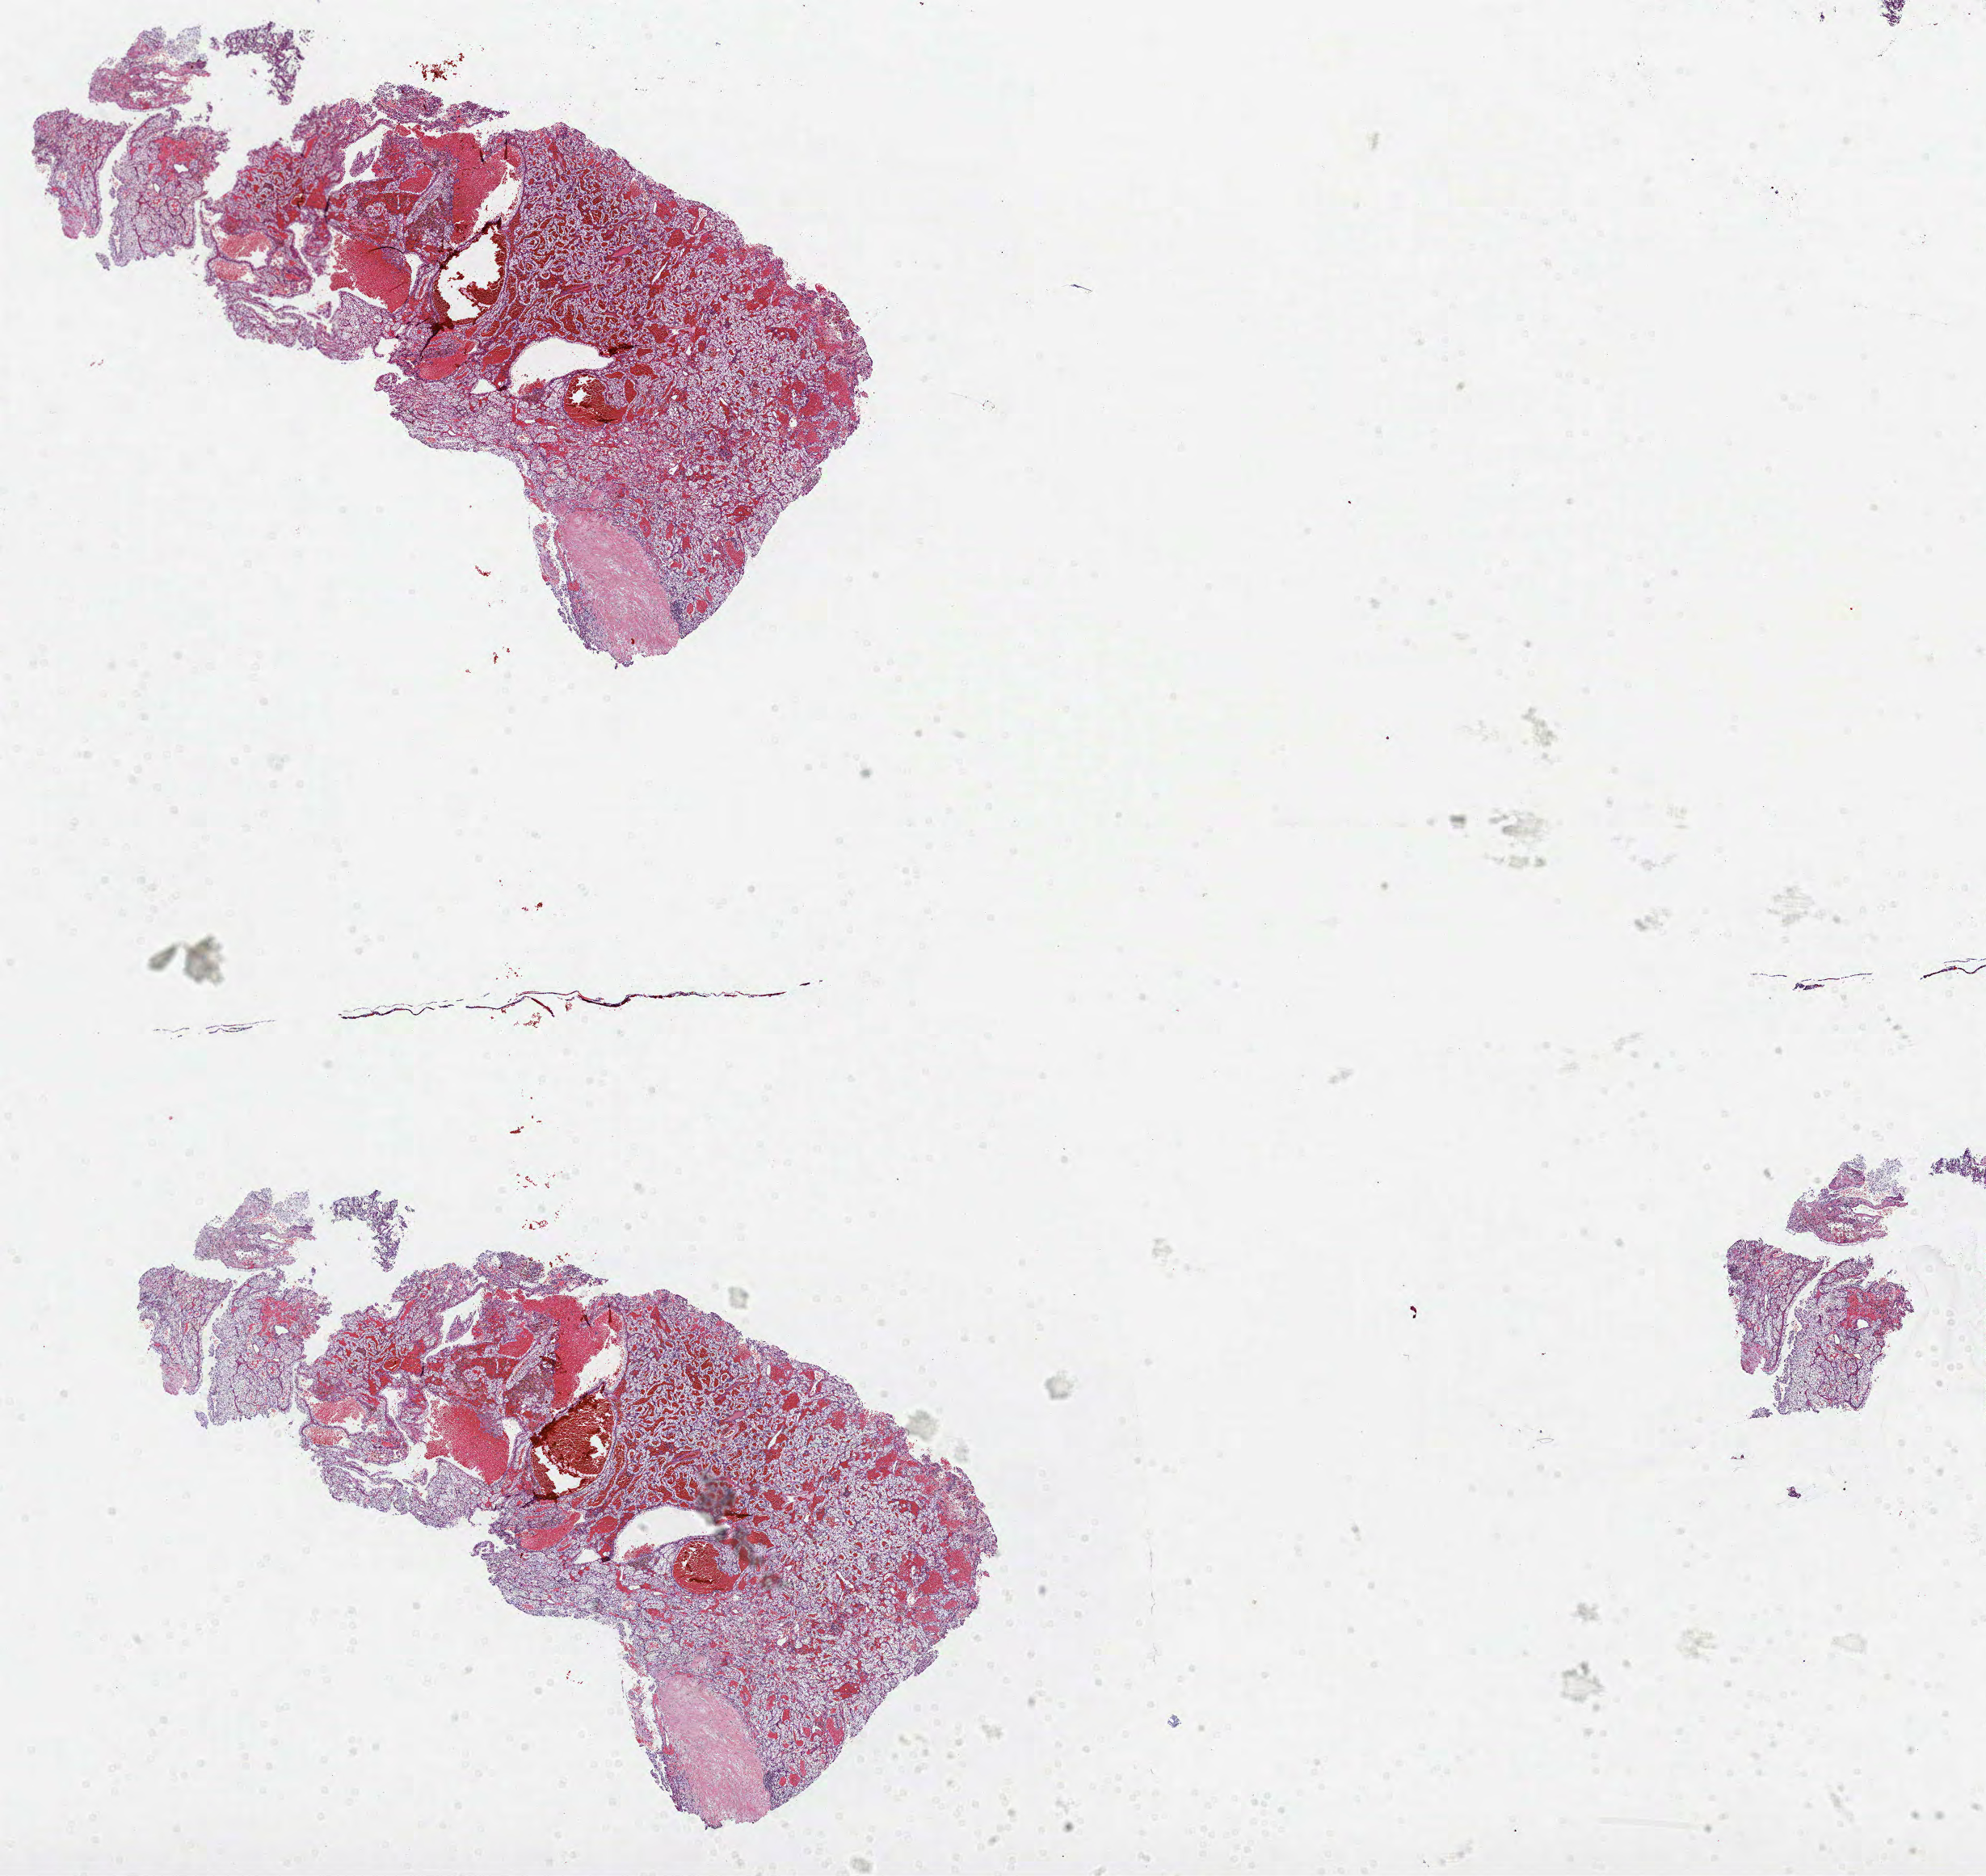
Hematoxylin and eosin (H&E) stained whole-slide image — shown as a low-resolution overview of the whole scanned area (about 19.8 x 18.7 mm); formalin-fixed paraffin-embedded (FFPE) diagnostic section; kidney, primary tumour sample. Patient: male, age at initial diagnosis 56 years. Histologic grade: G2 (moderately differentiated).
TNM: T1b N0 M0. Pathologic diagnosis: Clear cell adenocarcinoma, NOS. AJCC pathologic stage: I.